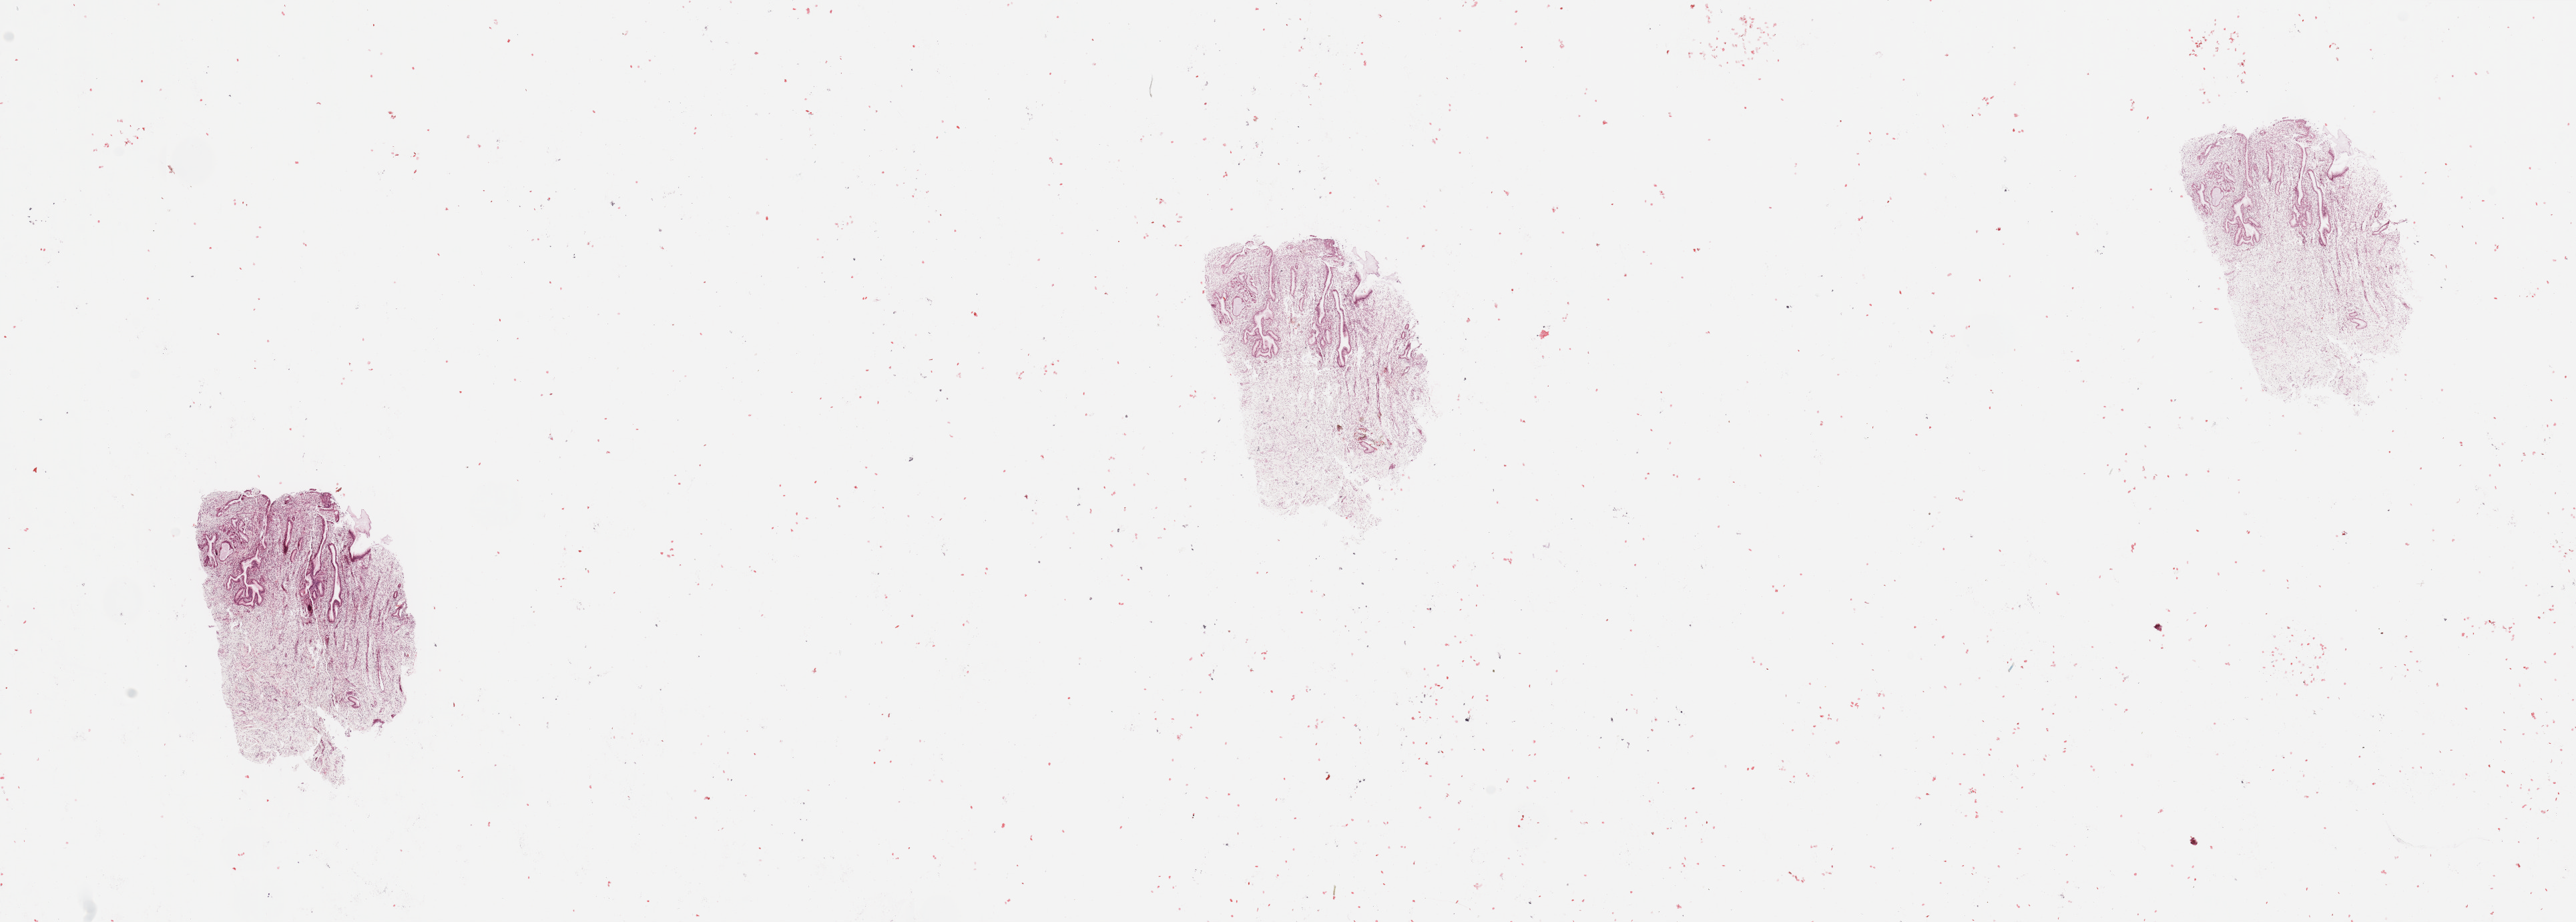
Digitized Hematoxylin and eosin (H&E) stained tissue section (whole slide), shown as a low-resolution overview of the whole scanned area (about 30.5 x 10.9 mm, from a 20x scan), normal (non-tumour) tissue sample, uterus. Patient: female, age 67 years.
* this section: normal (non-tumour) tissue from the same patient
* patient diagnosis: Endometrioid adenocarcinoma, NOS